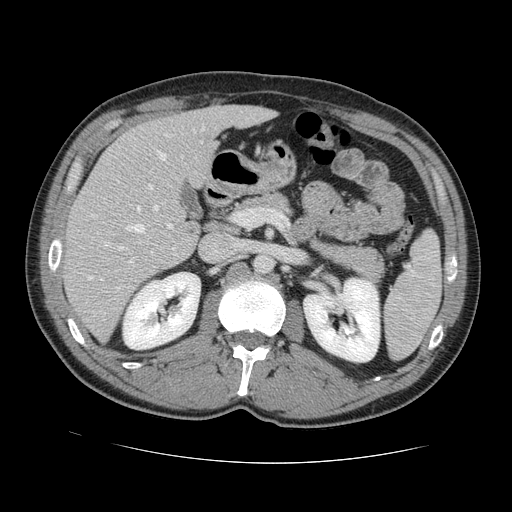
Contrast-enhanced abdominal CT, one axial slice. Position 72 of 131 along the scan axis. 120 kVp. Intravenous contrast given. Soft-tissue window (W 400 / L 40 HU). 2.5 mm slice thickness. 512 × 512 image matrix, field of view 380 × 380 mm. Male patient, age 40 years. From the clinical record (not read from this slice): diagnosis: colorectal cancer liver metastases, imaged before liver resection; multiple liver metastases: yes; largest metastasis: 2.9 cm; disease in both lobes: yes.
Annotated regions visible in this slice (expert manual segmentation):
- hepatic veins: bounding box [x1, y1, x2, y2] px = [88, 150, 167, 281]
- liver: [66, 107, 270, 340]
- planned liver remnant (the part of the liver to remain after resection): [107, 106, 270, 192]
- portal vein (with intrahepatic branches): [128, 184, 173, 264]
- liver metastasis: [189, 228, 194, 235]